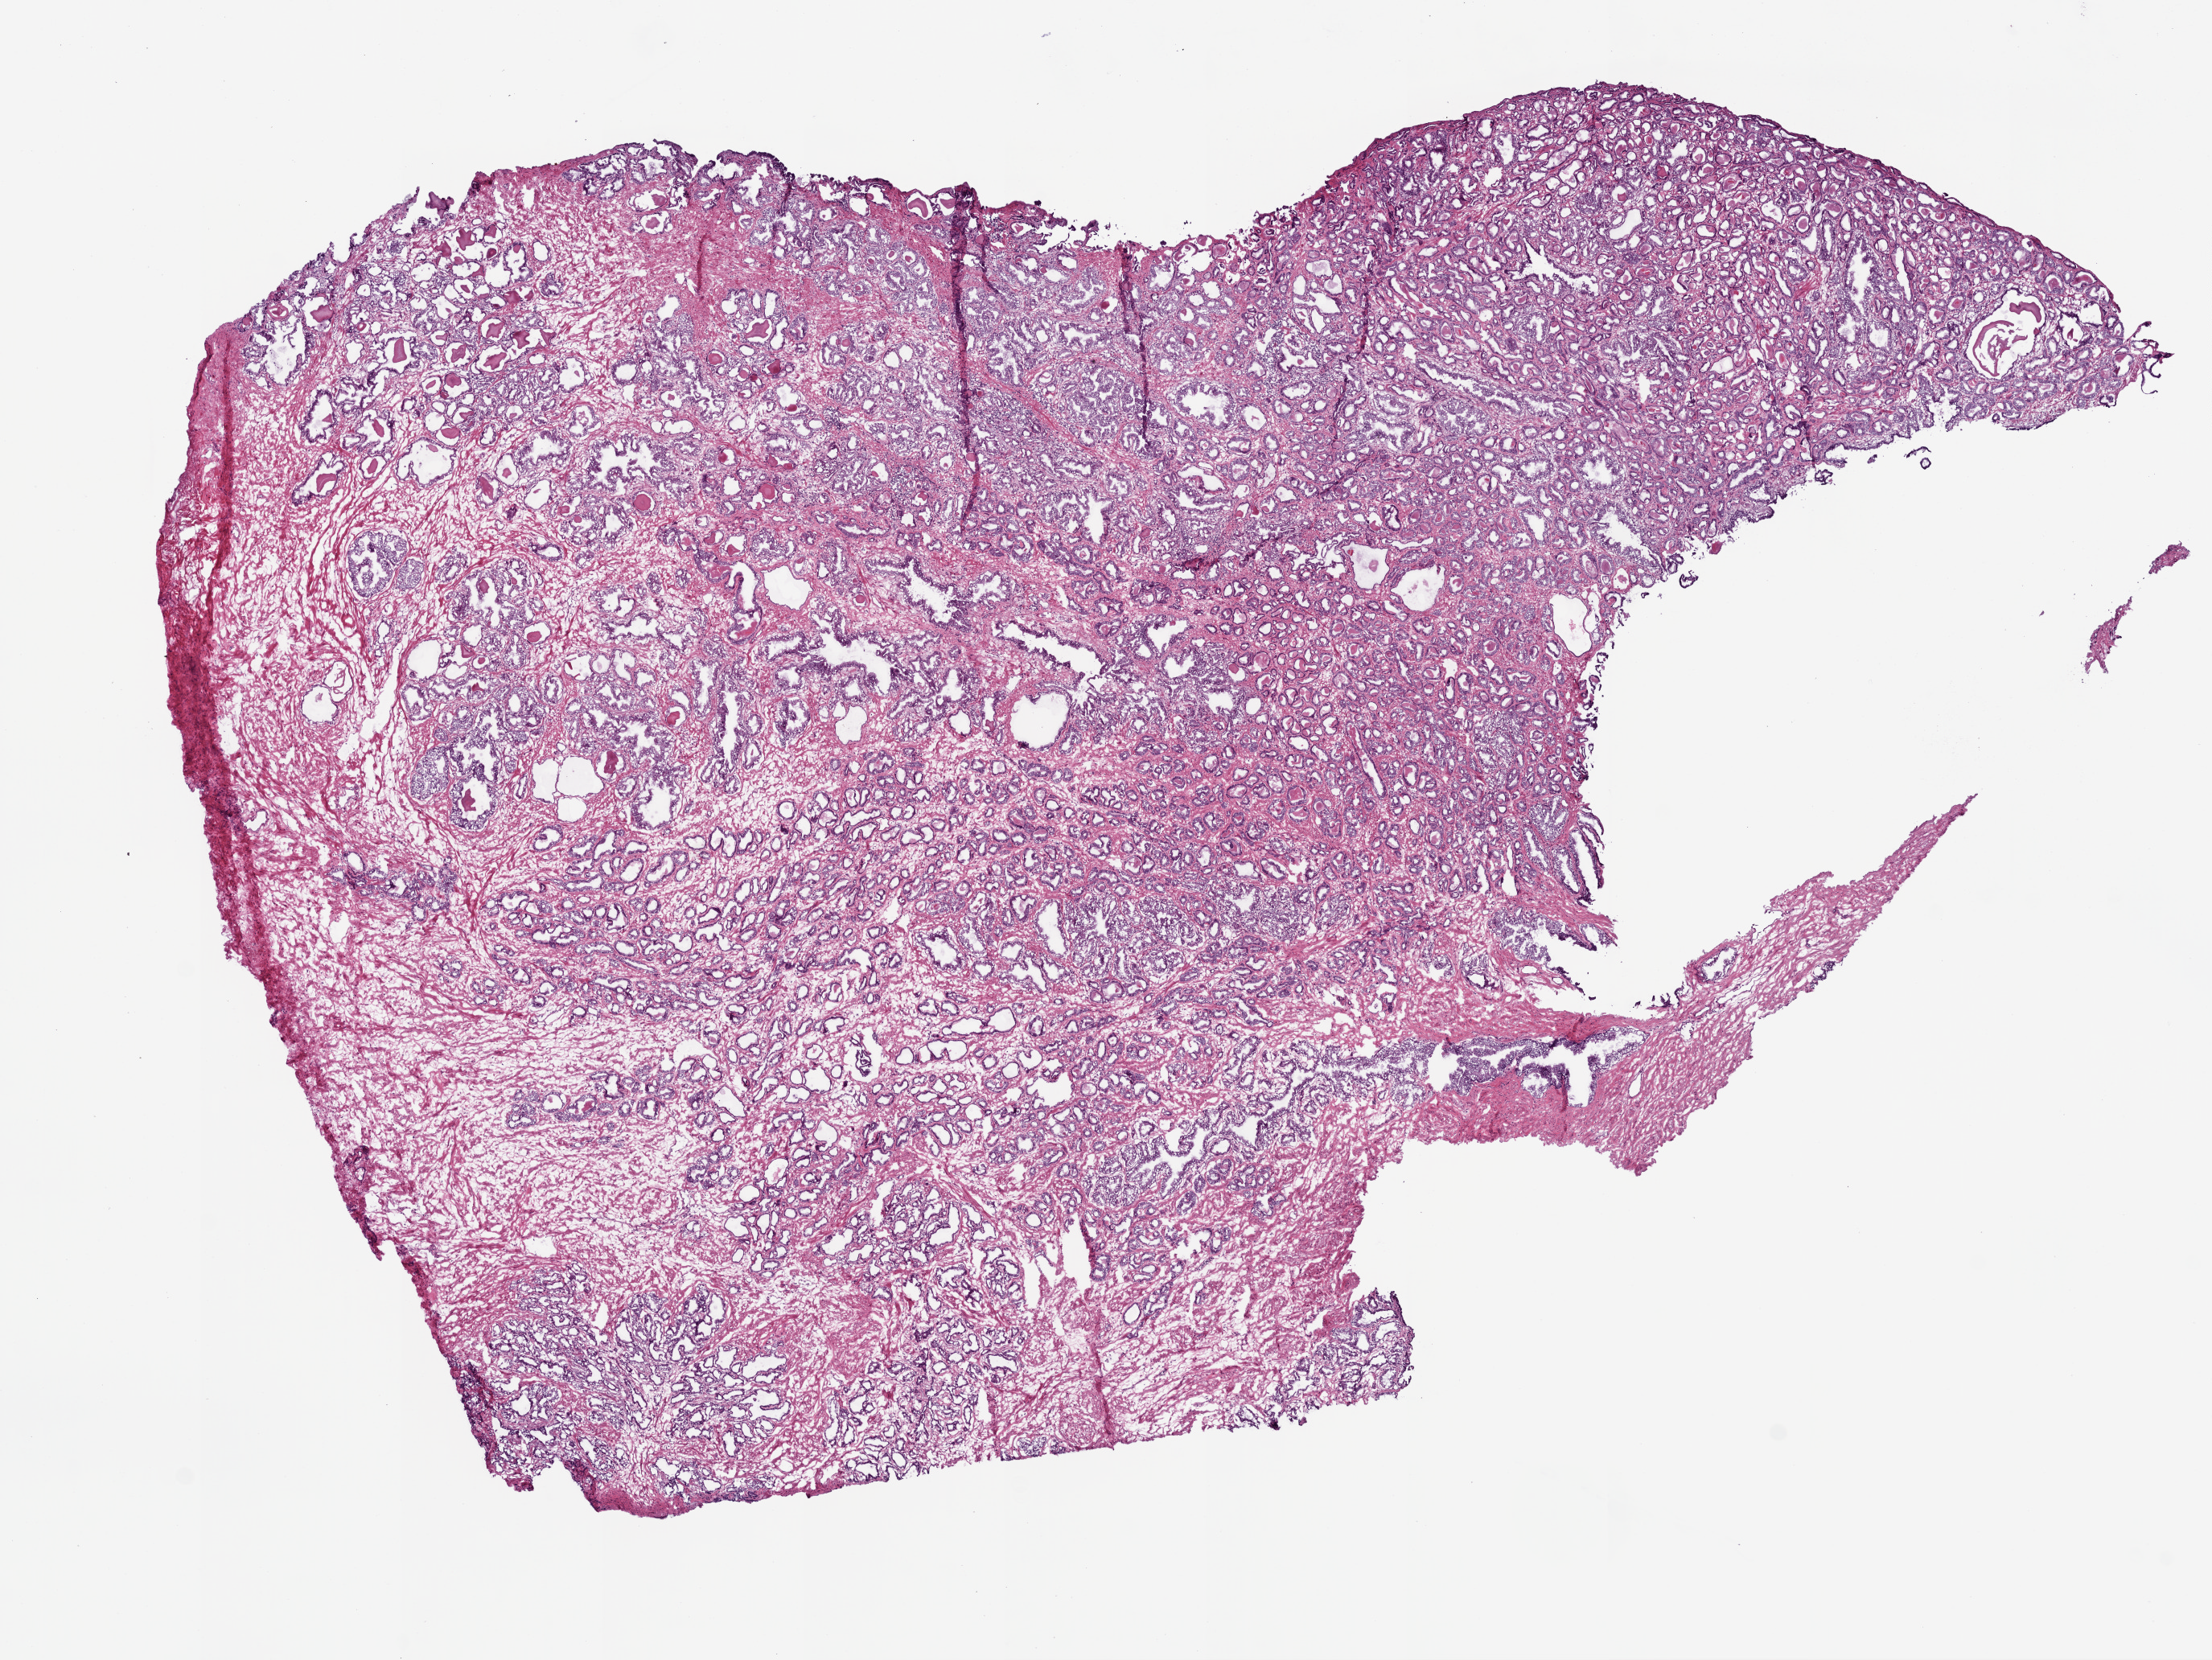
Digitized Hematoxylin and eosin (H&E) stained tissue section (whole slide) — shown as a low-resolution overview of the whole scanned area (about 11.0 x 8.3 mm, from a 20x scan), frozen section from the top of the tissue portion, sample: primary tumour, prostate. Male, age 46 years at initial diagnosis. Gleason score: 7 (3+4). Composition of this section per pathologist review: tumour cells 50%, tumour nuclei 65%, normal cells 20%, stromal cells 30%, necrosis 0%. Inflammatory infiltration, as recorded: lymphocyte infiltration 1%, monocyte infiltration 0%, neutrophil infiltration 0%.
* laterality: bilateral
* lymph nodes positive (case pathology): 0 of 13 examined
* diagnosis: Acinar cell carcinoma (prostate gland)